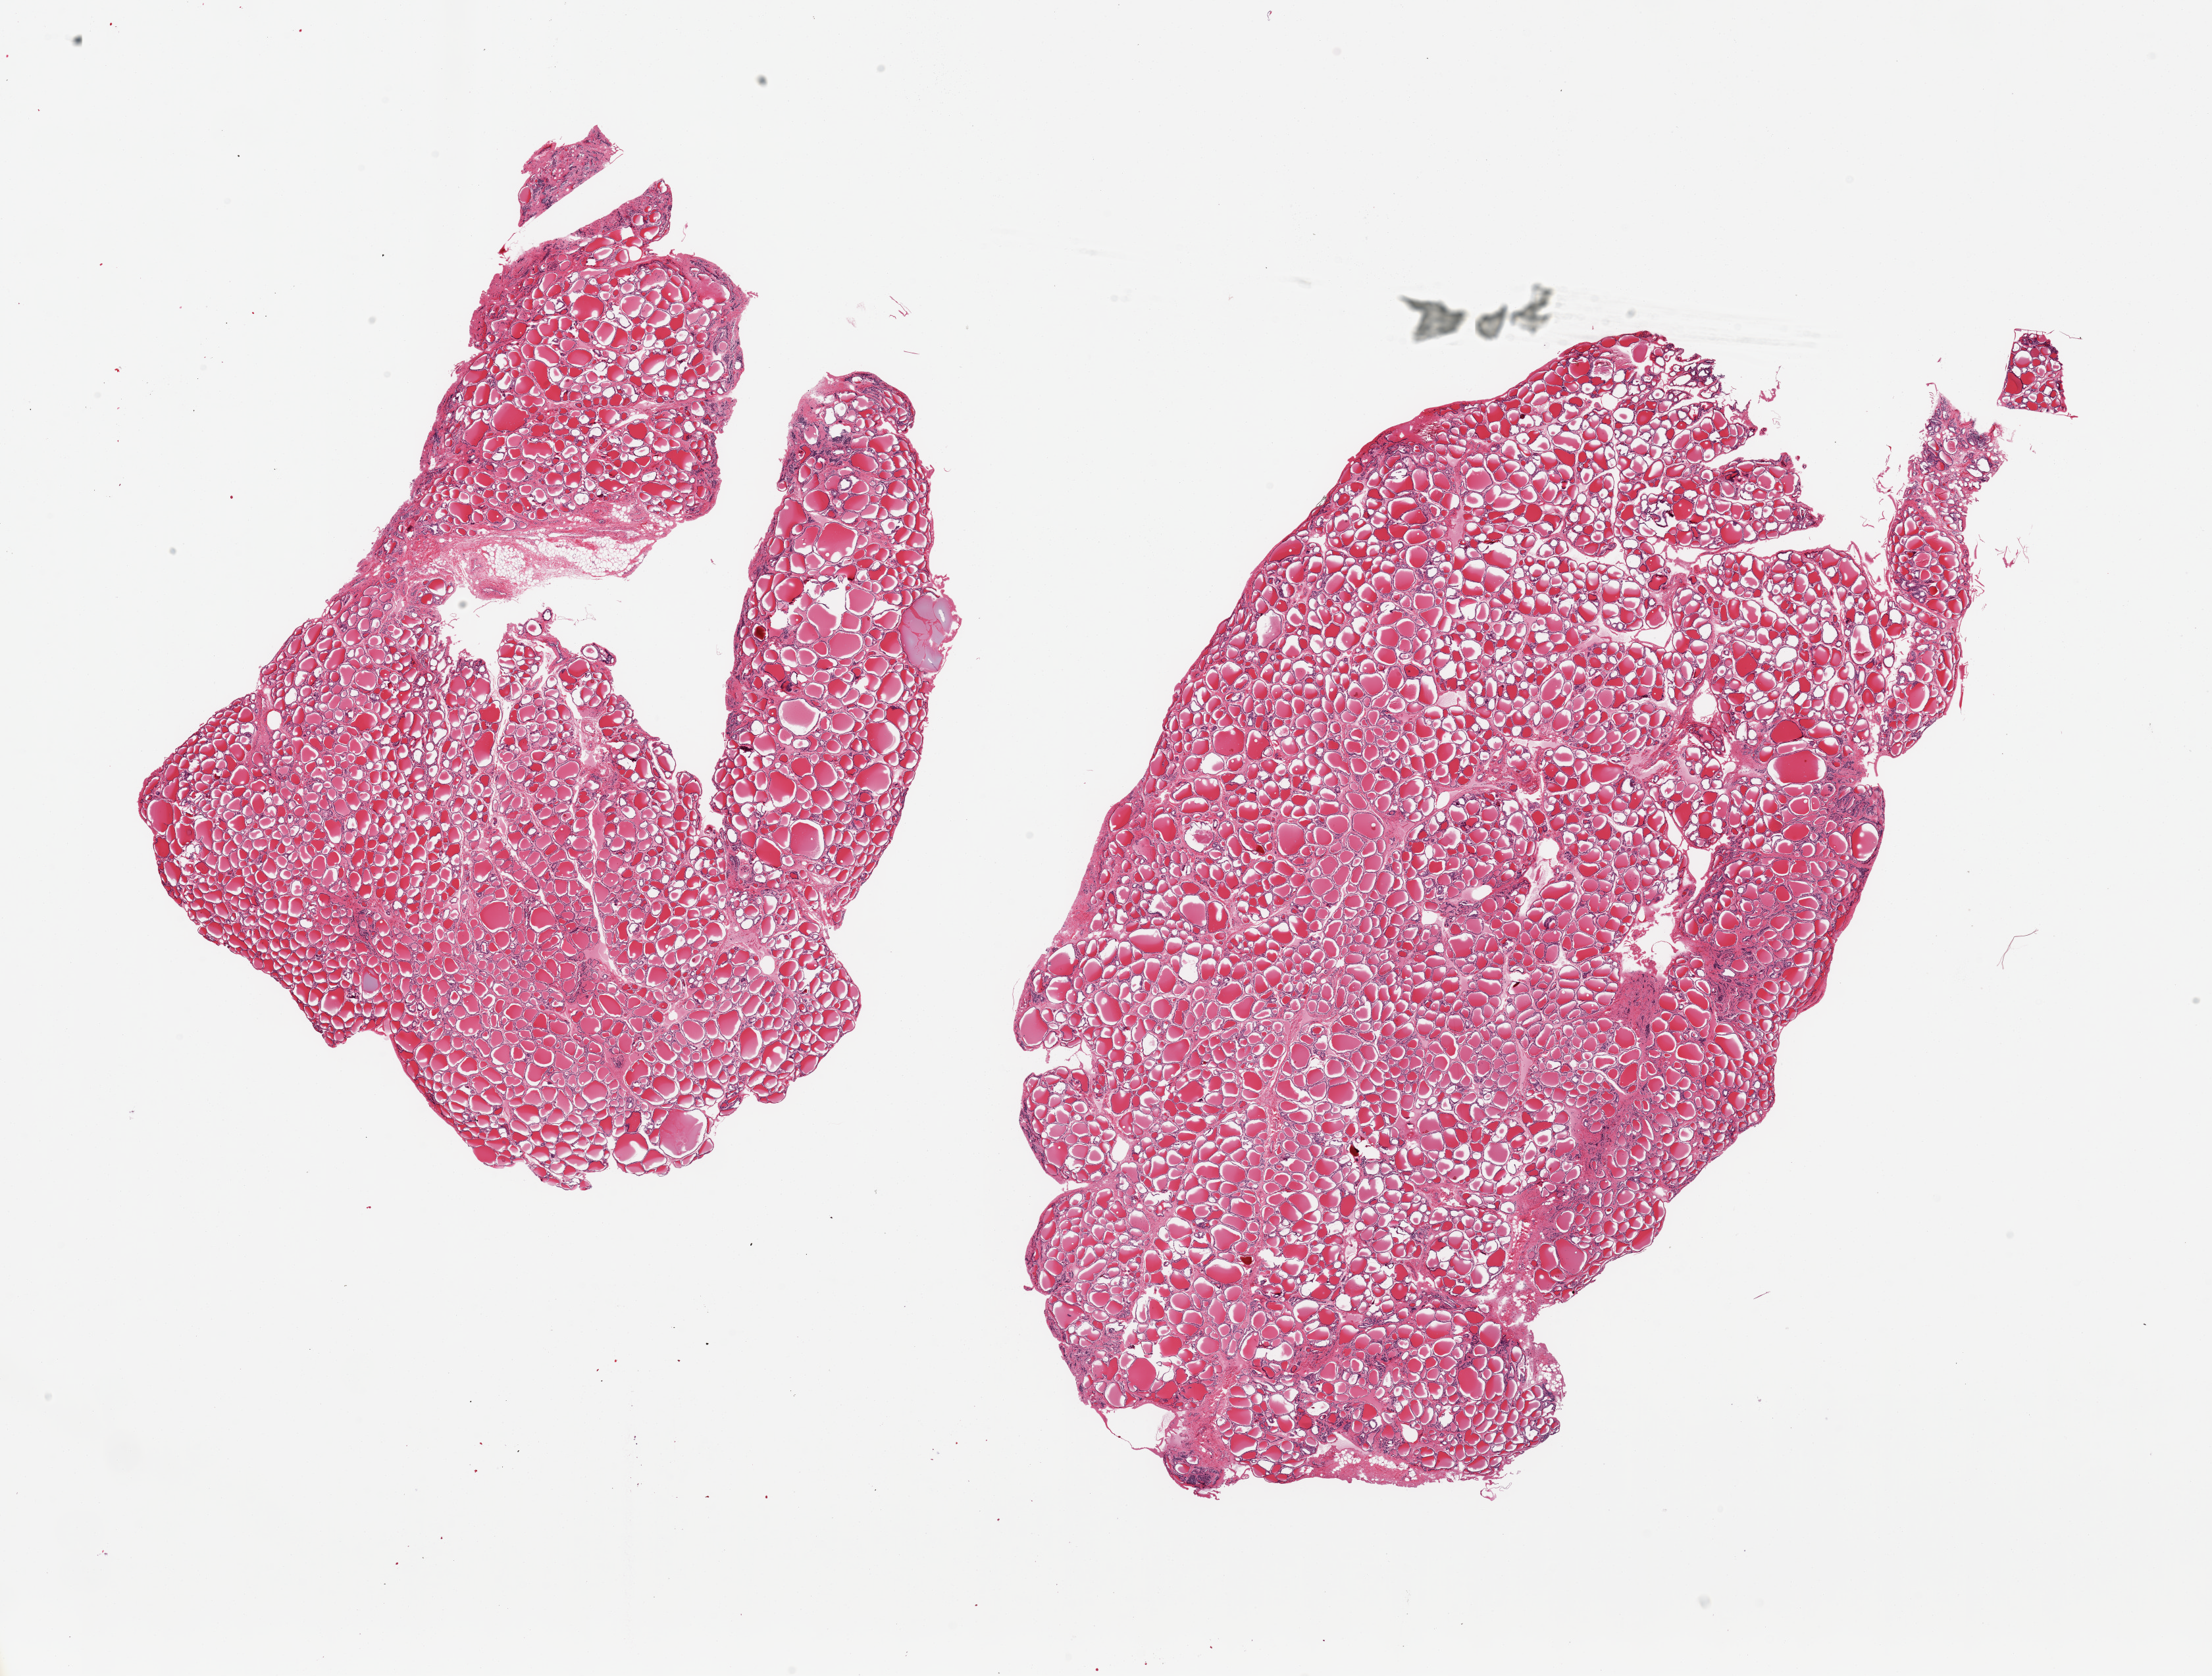
H&E whole-slide image — shown as a low-resolution overview of the whole scanned area (about 26.6 x 20.1 mm, slide scanned at 20x). PAXgene-fixed paraffin-embedded (PFPE) section. Target tissue: thyroid. Tissue donor sample. Donor sex: male.
Pathologist's review note for this sample: 2 pieces; trivial attachment of fat.